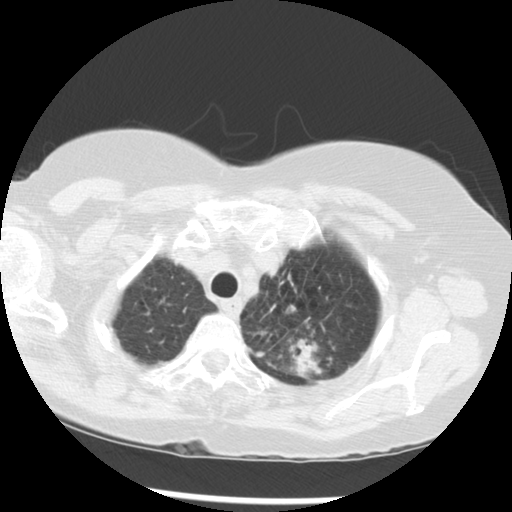
Low-dose screening chest CT, axial slice; third screening round (two years after baseline); lung window (W 1500 / L -600 HU); slice 243 of 283 in the series. Female participant, aged 70 years at enrolment.
Expert-annotated lung lesion, box from (x=246, y=292) to (x=345, y=380) px. The exam's reader record, not a measurement of the box and not confirmed to be the same lesion: non-calcified nodule or mass ≥4 mm, left upper lobe, 32 × 26 mm, spiculated (stellate) margins, soft tissue attenuation, pre-existing on the prior screen: yes; interval growth: yes.